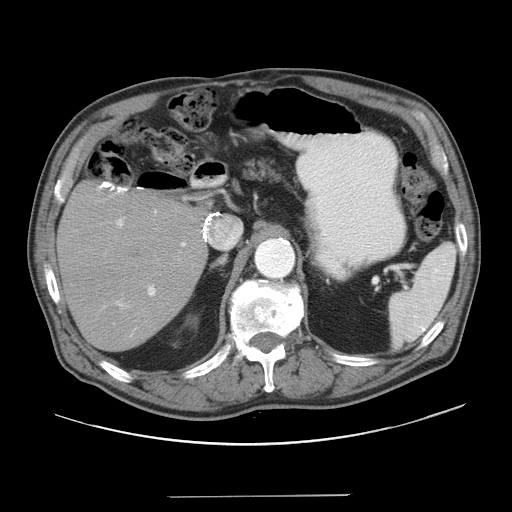
Contrast-enhanced abdominal CT, one axial slice. Position 26 of 41 along the scan axis. Reconstruction kernel STANDARD. Intravenous contrast given. Soft-tissue window (W 400 / L 40 HU). 5 mm slice thickness. 512 × 512 image matrix. Male patient, age 75 years. From the clinical record (not read from this slice): diagnosis: colorectal cancer liver metastases, imaged before liver resection; multiple liver metastases: no; largest metastasis: 5.2 cm; disease in both lobes: no.
Structures marked on this image (outlined manually by an expert reader):
- liver: bounding box (x1, y1, x2, y2) in pixels: (60, 186, 205, 351)
- planned liver remnant (the part of the liver to remain after resection): (60, 186, 205, 351)
- portal vein (with intrahepatic branches): (112, 209, 187, 325)